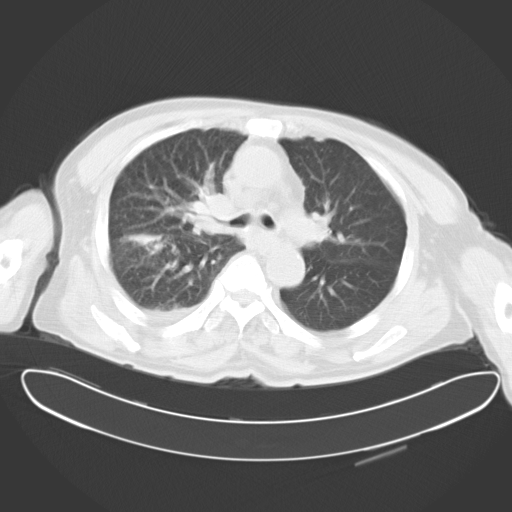
Chest CT, one axial slice; slice 19 of 30 in the series (ordered by position); 120 kVp; lung window (W 1500 / L -600 HU); 10 mm slice thickness; 512 × 512 image matrix, field of view 427 × 427 mm. Patient: male, 78 years. Case-level facts recorded for this patient, not image findings: clinical TNM (as recorded): T2 N1 M1.
Outlined on this slice (rectangle marked by the reading radiologist):
- lung tumour (recorded histology: adenocarcinoma): box from (x=116, y=179) to (x=231, y=266) px